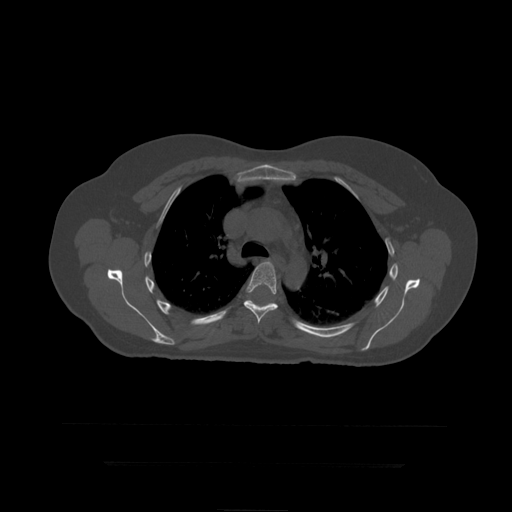
CT including the spine, one axial slice; slice 318 of 399 in the series (ordered by position); bone window (W 1800 / L 400 HU); 512 × 512 image matrix, field of view 450 × 450 mm. Patient age 41 years. From the clinical record (not read from this slice): primary cancer: breast.
Outlined on this slice (semi-automatically segmented with operator editing):
- T6 vertebra: bounding box (x1, y1, x2, y2) in pixels: (244, 262, 278, 324)
- T7 vertebra: (247, 300, 275, 305)